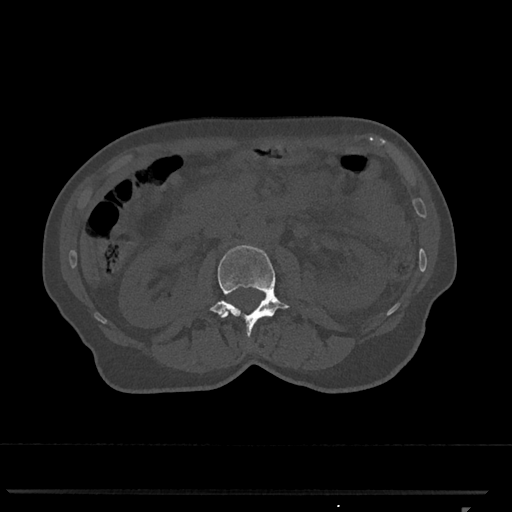
CT including the spine, one axial slice. Position 338 of 793 along the scan axis. Reconstruction kernel Br40s/3. Bone window (W 1800 / L 400 HU). 0.5 mm slice thickness. 512 × 512 image matrix, field of view 380 × 380 mm. Female patient, age 62 years. Case-level facts recorded for this patient, not image findings: primary cancer: renal.
Annotated regions visible in this slice (semi-automatically segmented with operator editing):
- L2 vertebra: bounding box <210,245,289,338> (left, top, right, bottom; pixels)